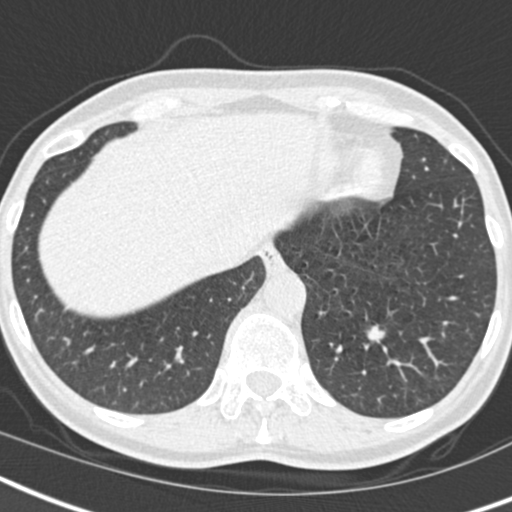
Low-dose screening chest CT, one axial slice; slice 45 of 173 in the series (ordered by position); 120 kVp; lung window (W 1500 / L -600 HU); 512 × 512 image matrix, field of view 293 × 293 mm.
Annotated regions visible in this slice (manually delineated by an expert):
- lesion 1 (tumor, lower lobe of left lung): box from (x=365, y=324) to (x=385, y=342) px